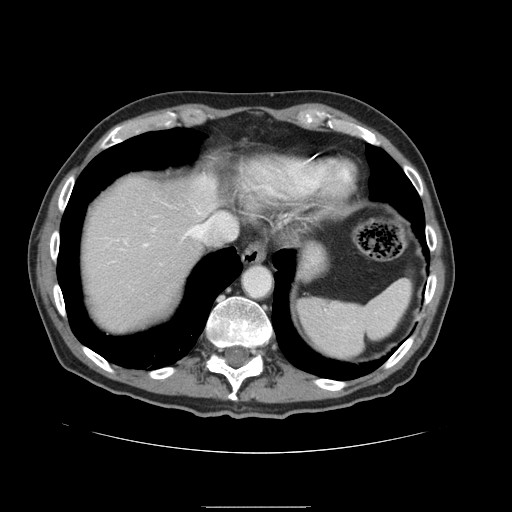
Contrast-enhanced abdominal CT, one axial slice; slice 130 of 168 in the series (ordered by position); 120 kVp; intravenous contrast given; soft-tissue window (W 400 / L 40 HU); 2.5 mm slice thickness; 512 × 512 image matrix, field of view 386 × 386 mm. Male patient, age 74 years. Case-level facts recorded for this patient, not image findings: diagnosis: colorectal cancer liver metastases, imaged before liver resection; multiple liver metastases: no; largest metastasis: 14.5 cm; chemotherapy before resection: no.
Outlined on this slice (expert manual segmentation):
- hepatic veins: bounding box [x1, y1, x2, y2] px = [188, 219, 223, 238]
- liver: [80, 172, 224, 333]
- planned liver remnant (the part of the liver to remain after resection): [80, 172, 223, 334]